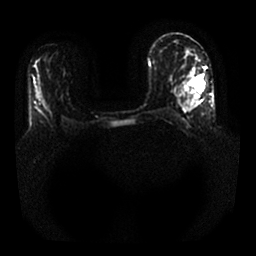
Breast MRI, one axial slice. Slice 12 of 25 in the series (ordered by position). Diffusion-weighted series; image 2 of 4 stored at this slice position (different b-values; order by instance number). 1.5 T. 4 mm slice thickness. 256 × 256 image matrix. Female patient.
Structures marked on this image (expert manual segmentation):
- tumour on diffusion-weighted imaging: bounding box (x1, y1, x2, y2) in pixels: (192, 76, 204, 91)